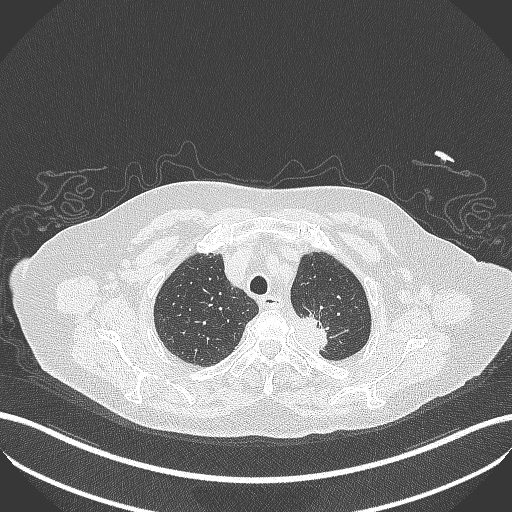
Chest CT, one axial slice. Position 286 of 353 along the scan axis. Reconstruction kernel B70f. 100 kVp. Lung window (W 1500 / L -600 HU). 1 mm slice thickness. 512 × 512 image matrix, field of view 400 × 400 mm. Female patient, age 81 years. From the clinical record (not read from this slice): clinical TNM (as recorded): T2a N0 M0.
Outlined on this slice (rectangle marked by the reading radiologist):
- lung tumour (recorded histology: adenocarcinoma): box from (x=287, y=306) to (x=334, y=353) px